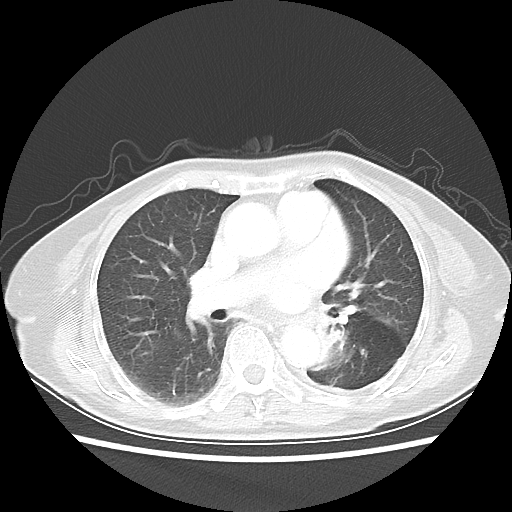
Chest CT, one axial slice; position 26 of 50 along the scan axis; reconstruction kernel LUNG; 80 kVp; lung window (W 1500 / L -600 HU); 512 × 512 image matrix, field of view 335 × 335 mm. Patient: female, 81 years. Case-level facts recorded for this patient, not image findings: clinical TNM (as recorded): T2 N0 M1a.
Structures marked on this image (rectangle marked by the reading radiologist):
- lung tumour (recorded histology: squamous cell carcinoma): bounding box <306,307,360,385> (left, top, right, bottom; pixels)